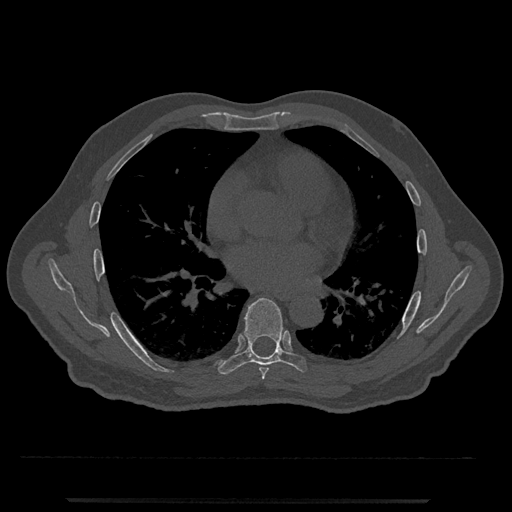
CT including the spine, one axial slice; position 695 of 797 along the scan axis; reconstruction kernel Br40s/3; 120 kVp; bone window (W 1800 / L 400 HU); 0.5 mm slice thickness; 512 × 512 image matrix, field of view 419 × 419 mm. Patient: male, 63 years. Case-level facts recorded for this patient, not image findings: primary cancer: prostate.
Annotated regions visible in this slice (semi-automatically segmented with operator editing):
- T6 vertebra: bounding box [x1, y1, x2, y2] px = [259, 367, 269, 380]
- T7 vertebra: [218, 298, 308, 375]